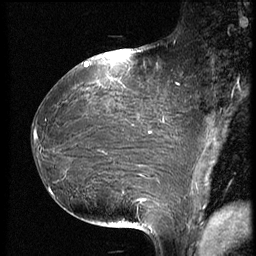
Breast MRI (dynamic contrast-enhanced), one sagittal slice; position 33 of 66 along the scan axis; dynamic contrast-enhanced series, image 2 of 3 at this slice position (ordered by acquisition); 1.5 T; TE 4.2 ms, TR 8.9 ms; 256 × 256 image matrix. Patient: female, 39 years. From the clinical record (not read from this slice): setting: breast cancer imaged before/during neoadjuvant chemotherapy; receptor status: HER2-positive.
Structures marked on this image (semi-automatically segmented with operator editing):
- analysis volume of interest (the breast-tissue region the enhancement analysis was run in; not a lesion): bounding box [x1, y1, x2, y2] px = [32, 75, 188, 218]
- tumour enhancement mask (voxels above the 140 % enhancement threshold inside the analysis volume of interest): [34, 131, 145, 204]